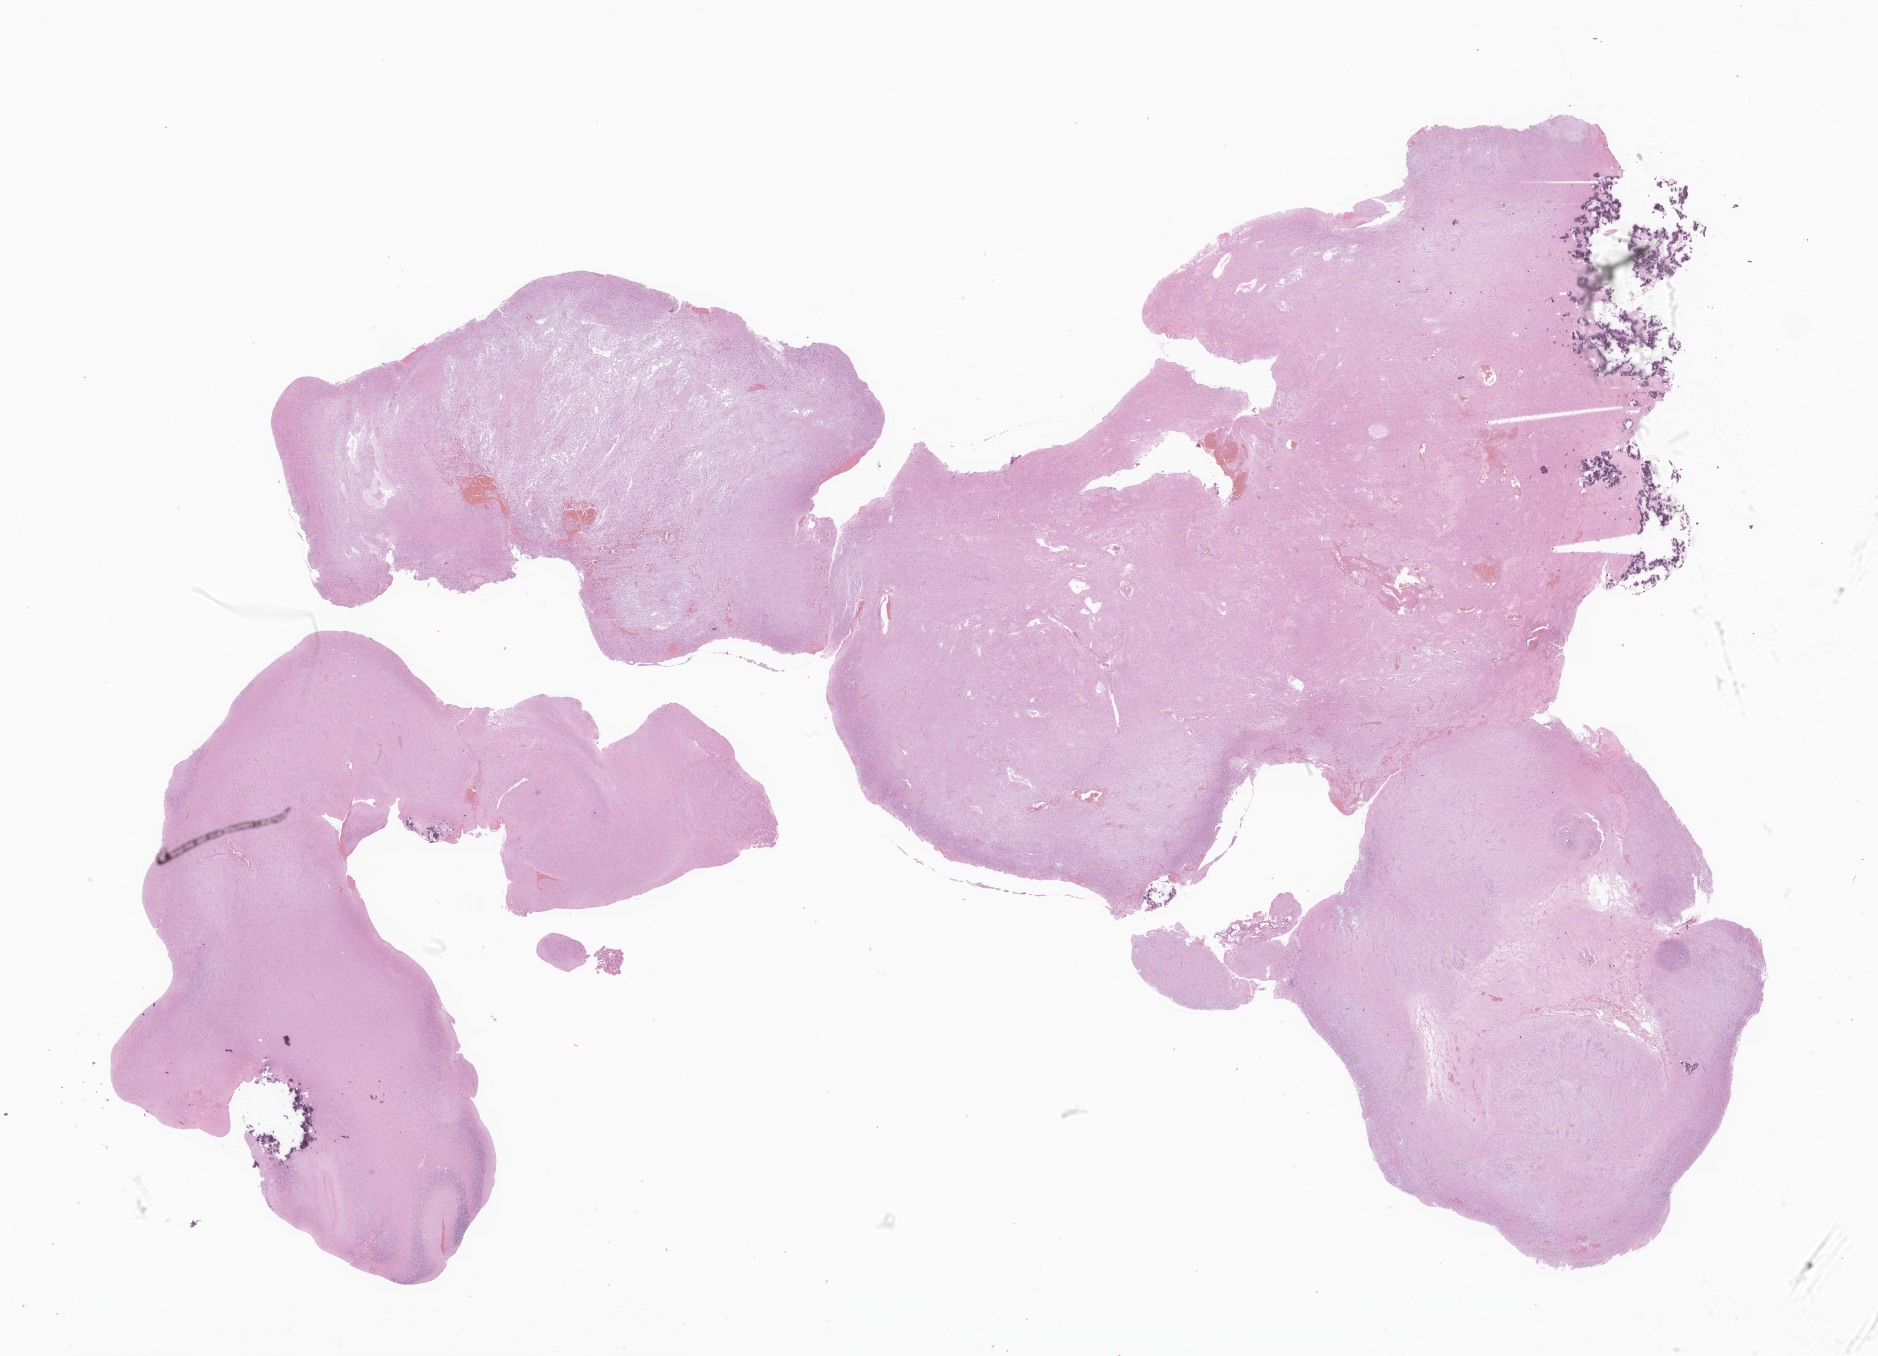
Digitized H&E-stained section of tumor tissue from the brain, shown as a low-resolution overview of the whole scanned area (about 31.7 x 22.9 mm); formalin-fixed, paraffin-embedded (FFPE) tissue. Patient female; age 128 months (10 years 8 months).
Recorded diagnosis: Neoplasm, malignant.